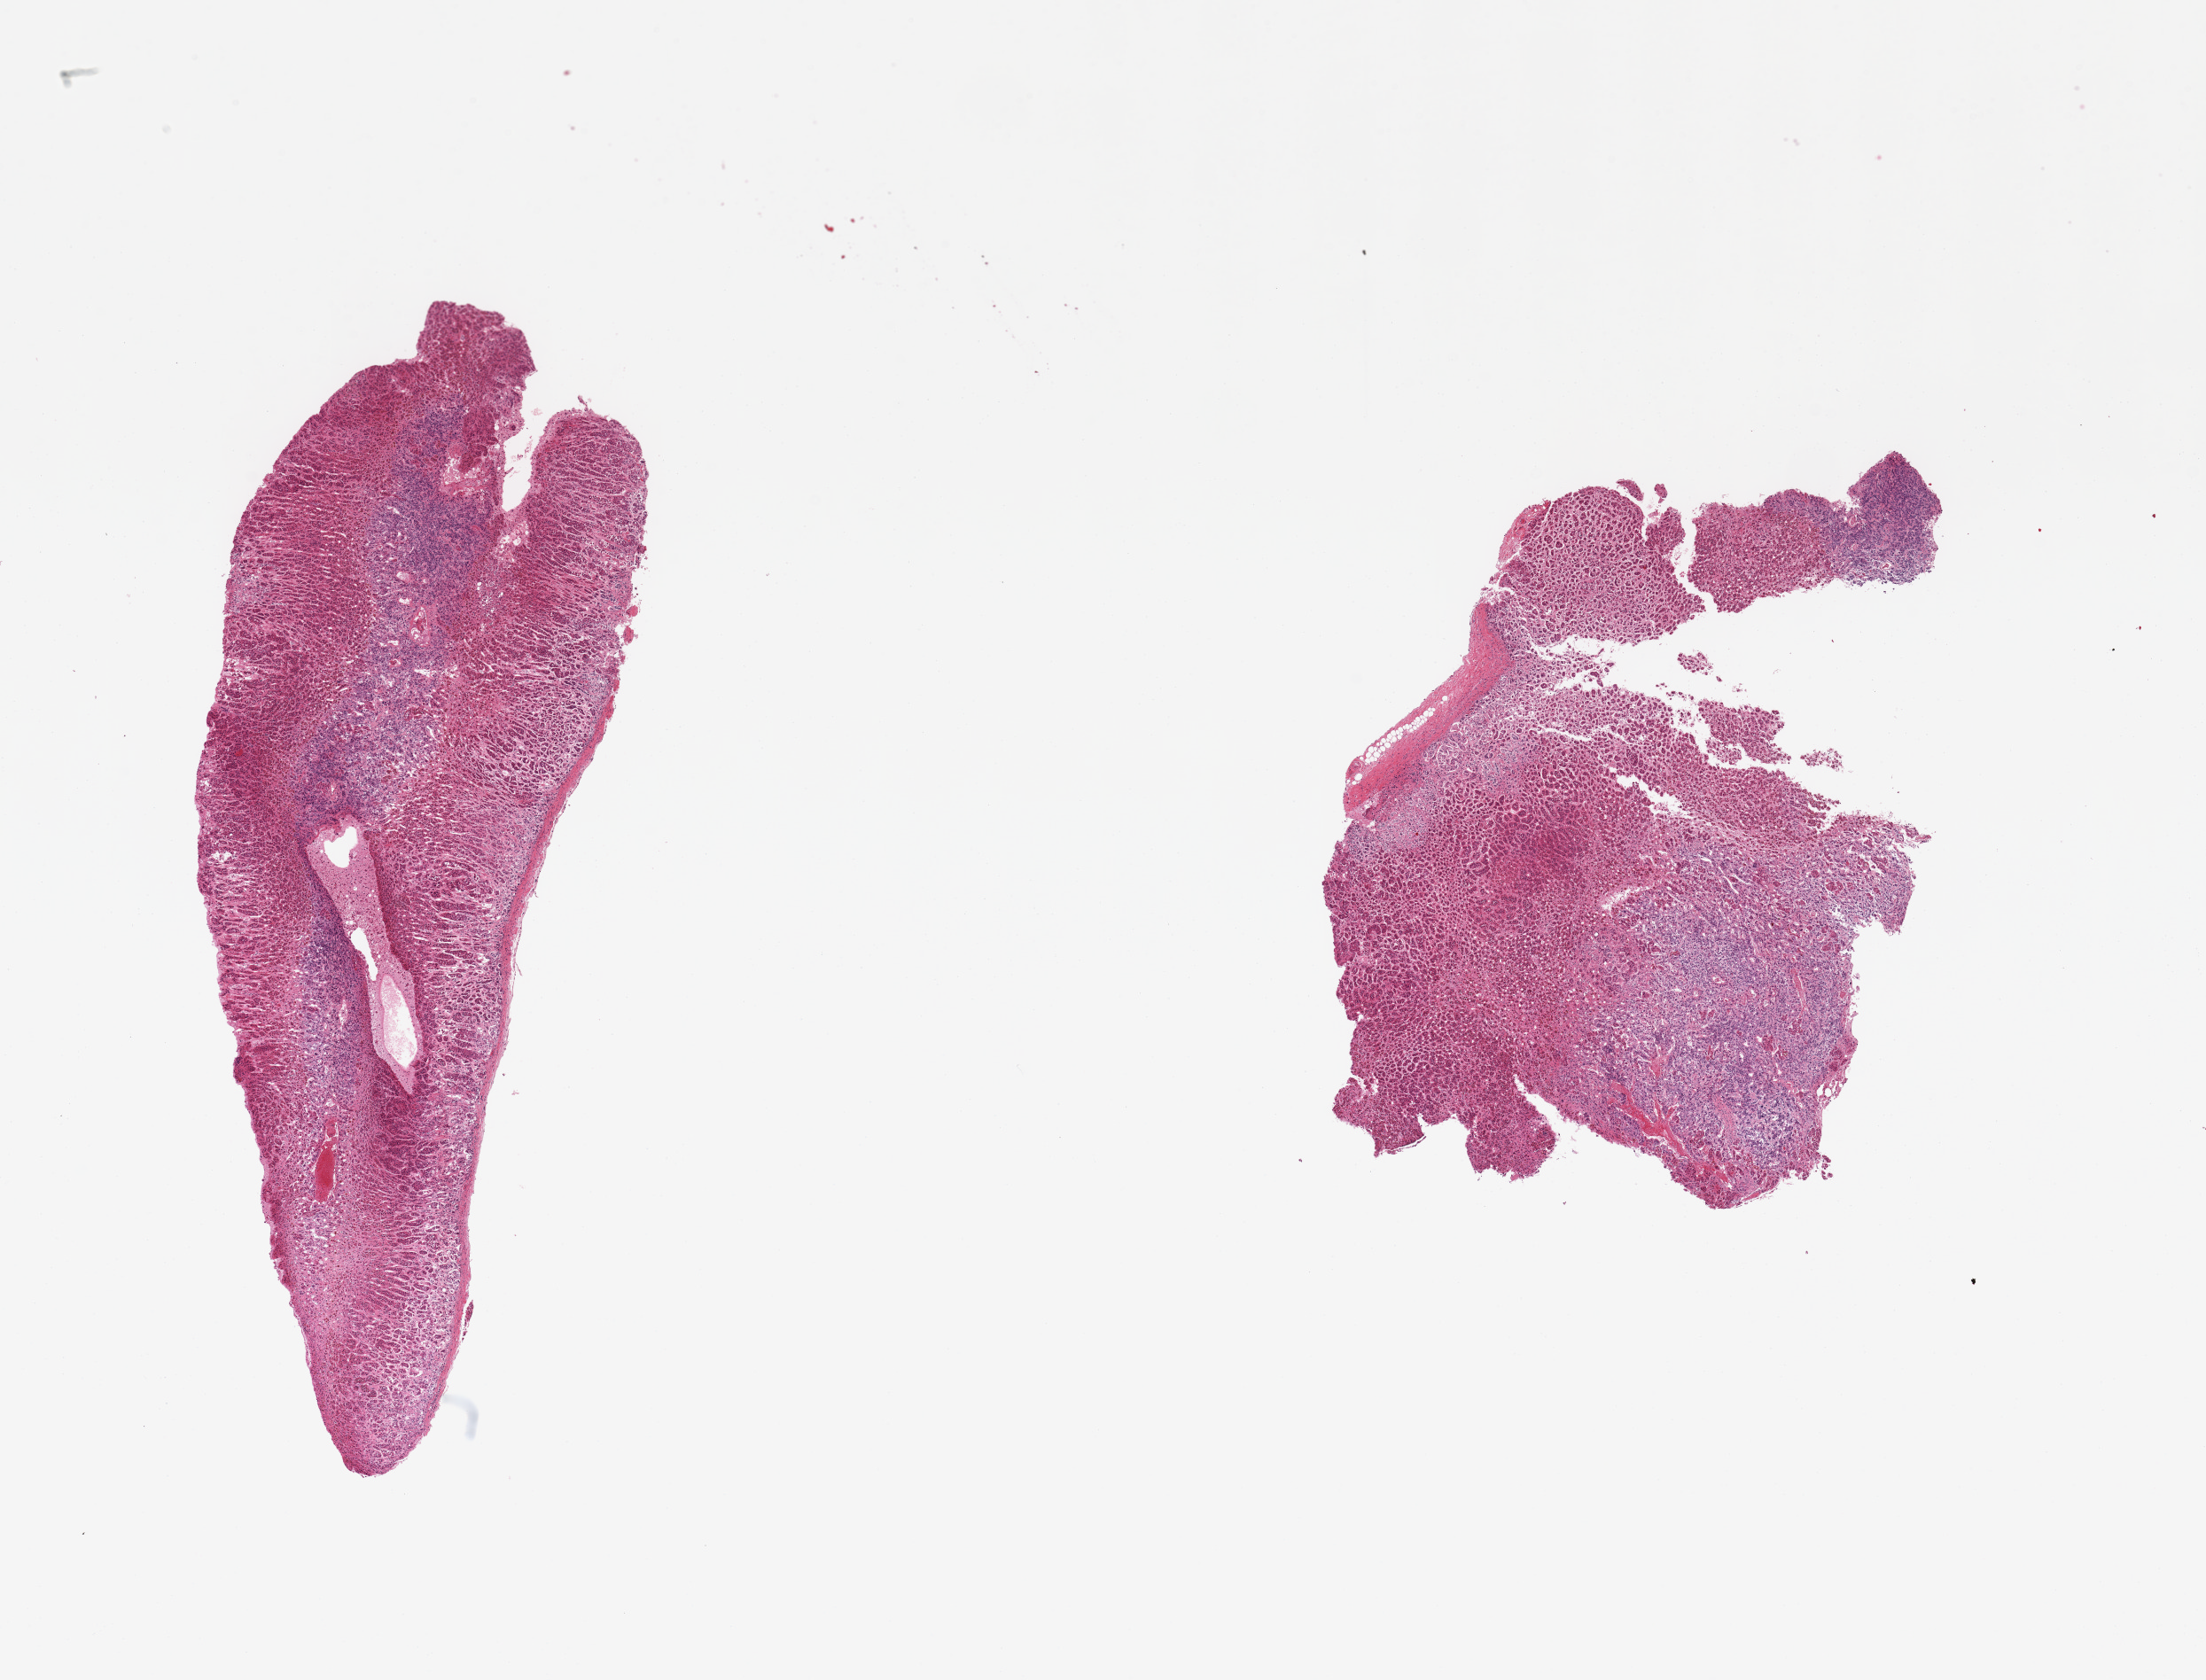
Hematoxylin and eosin (H&E) whole-slide image — whole scanned area (about 19.7 x 15.0 mm, acquisition: 20x scan) shown as a low-resolution overview; PAXgene-fixed paraffin-embedded (PFPE) section; section of adrenal gland (target tissue); donor tissue sample. Donor: male.
Pathologist's review note for this sample: 2 pieces; well dissected; no extraneous fat.